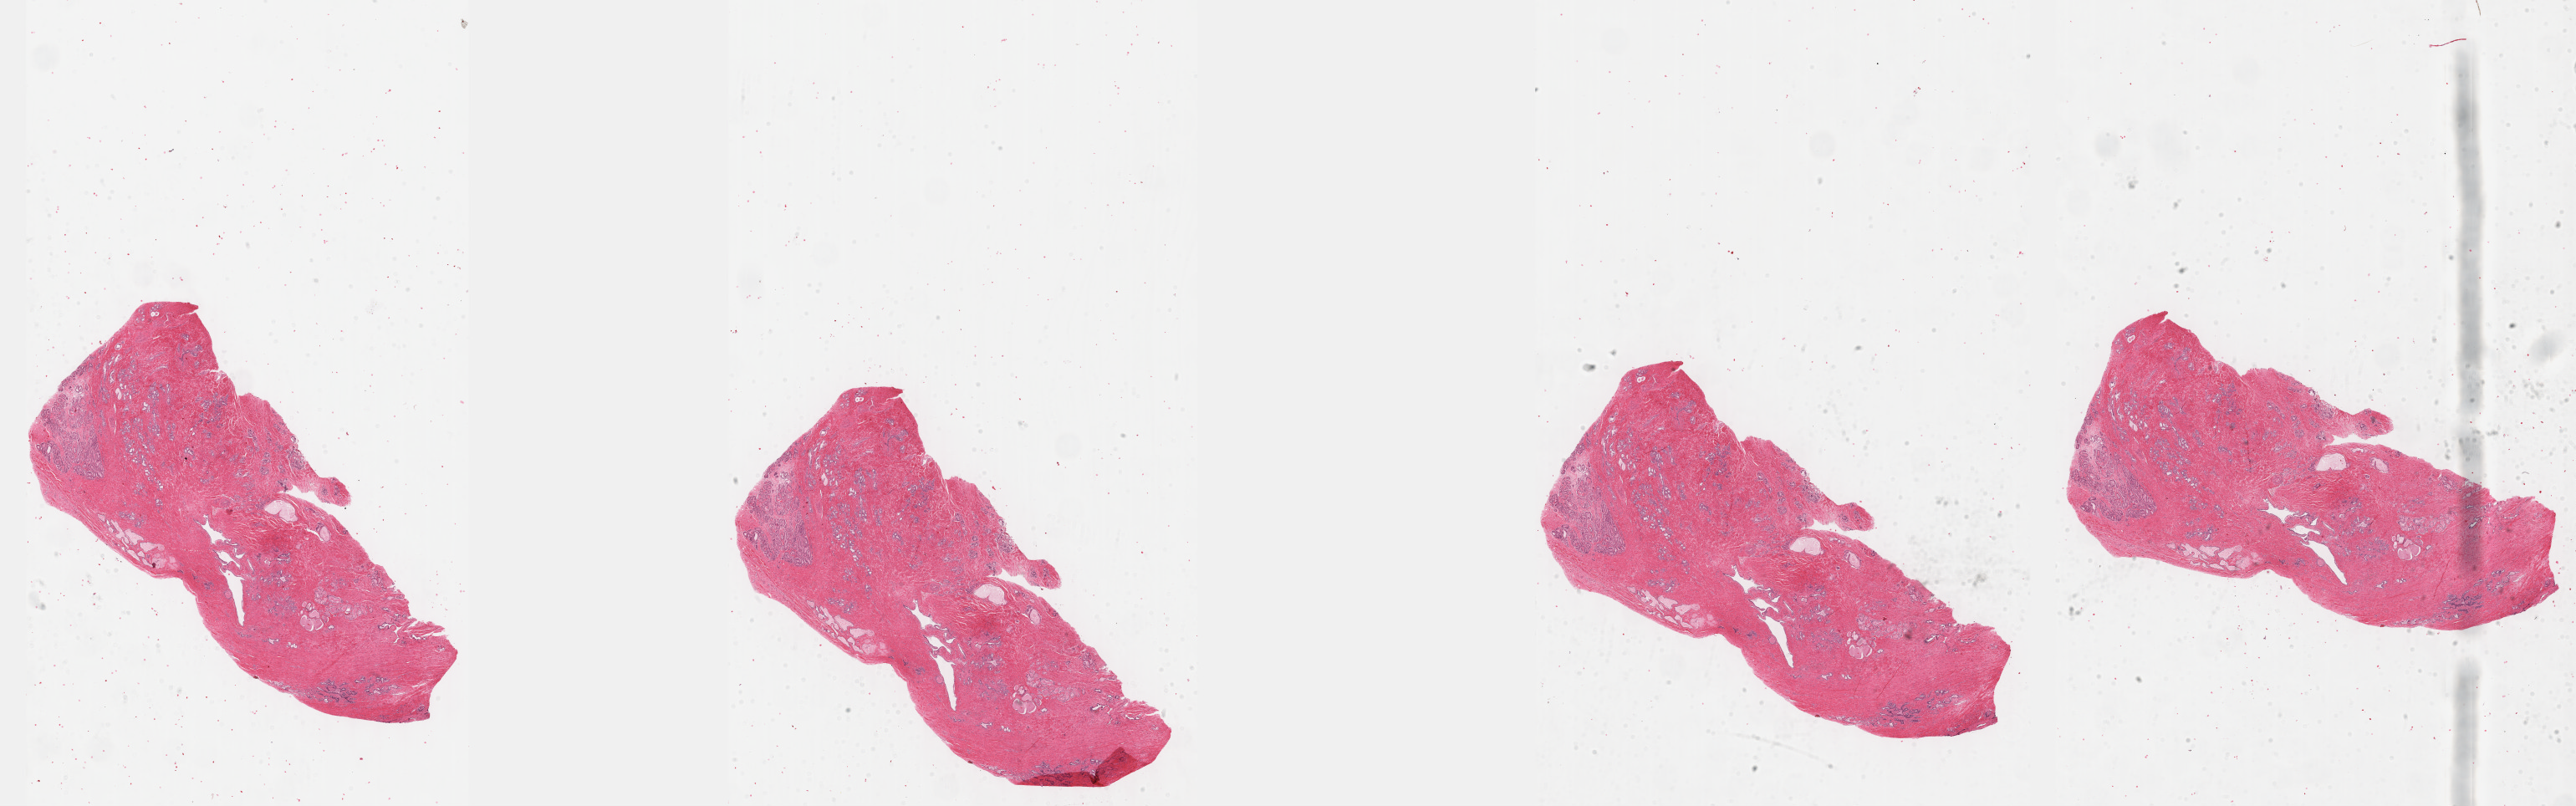
Whole-slide histology image, H&E-stained — low-resolution overview of the scanned area, about 49.8 x 15.6 mm (from a 40x scan); FFPE section; prostate, primary tumour sample. Male, age 68 years at initial diagnosis.
Histologic diagnosis: Adenocarcinoma, NOS (prostate gland).